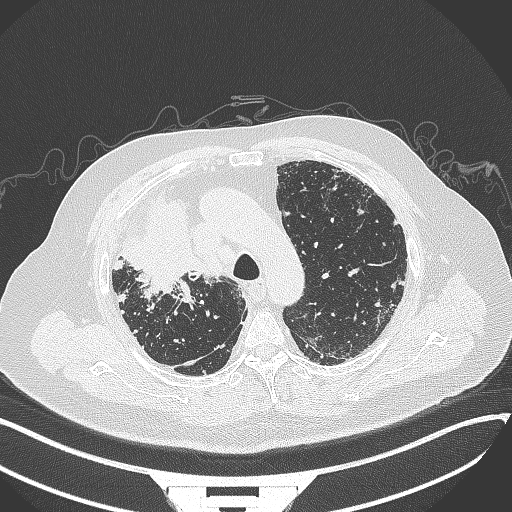
Chest CT, one axial slice; slice 262 of 384 in the series (ordered by position); reconstruction kernel B70f; 120 kVp; lung window (W 1500 / L -600 HU); 512 × 512 image matrix, field of view 400 × 400 mm. Patient: male, 69 years. Case-level facts recorded for this patient, not image findings: clinical TNM (as recorded): T4 N3 M1.
Structures marked on this image (rectangle marked by the reading radiologist):
- lung tumour (recorded histology: adenocarcinoma): bounding box [x1, y1, x2, y2] px = [118, 193, 225, 307]